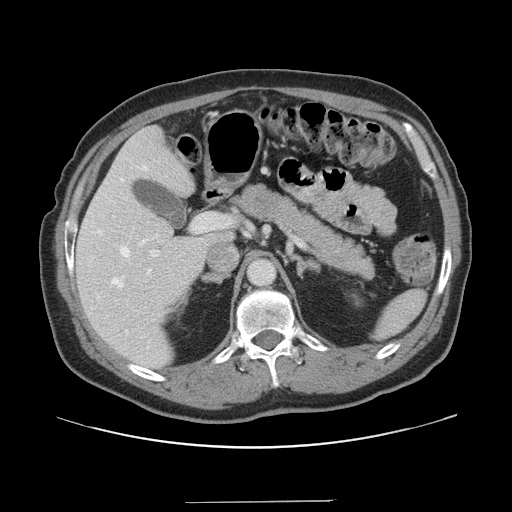
Contrast-enhanced abdominal CT, one axial slice. Slice 89 of 151 in the series (ordered by position). Intravenous contrast given. Soft-tissue window (W 400 / L 40 HU). 2.5 mm slice thickness. 512 × 512 image matrix. Male patient, age 63 years. Case-level facts recorded for this patient, not image findings: diagnosis: colorectal cancer liver metastases, imaged before liver resection; multiple liver metastases: no; largest metastasis: 2.1 cm; disease in both lobes: no.
Outlined on this slice (outlined manually by an expert reader):
- hepatic veins: box from (x=98, y=166) to (x=151, y=343) px
- liver: (x=76, y=128)–(x=230, y=369)
- planned liver remnant (the part of the liver to remain after resection): (x=76, y=128)–(x=230, y=369)
- portal vein (with intrahepatic branches): (x=150, y=213)–(x=231, y=257)